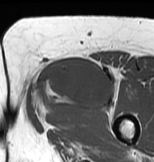
MRI of an extremity soft-tissue mass, one axial slice. Slice 37 of 83 in the series (ordered by position). MR volume resampled by the dataset authors to the PET/CT grid (not the native acquisition matrix). 154 × 162 image matrix. Female patient. Case-level facts recorded for this patient, not image findings: histological type: myxofibrosarcoma; grade: intermediate; site of the primary tumour: left thigh.
Outlined on this slice (expert contour drawn on MRI and transferred to this co-registered scan by the dataset authors):
- gross tumour volume including surrounding oedema: bounding box [x1, y1, x2, y2] px = [28, 55, 120, 122]
- gross tumour volume (mass): [33, 55, 111, 108]